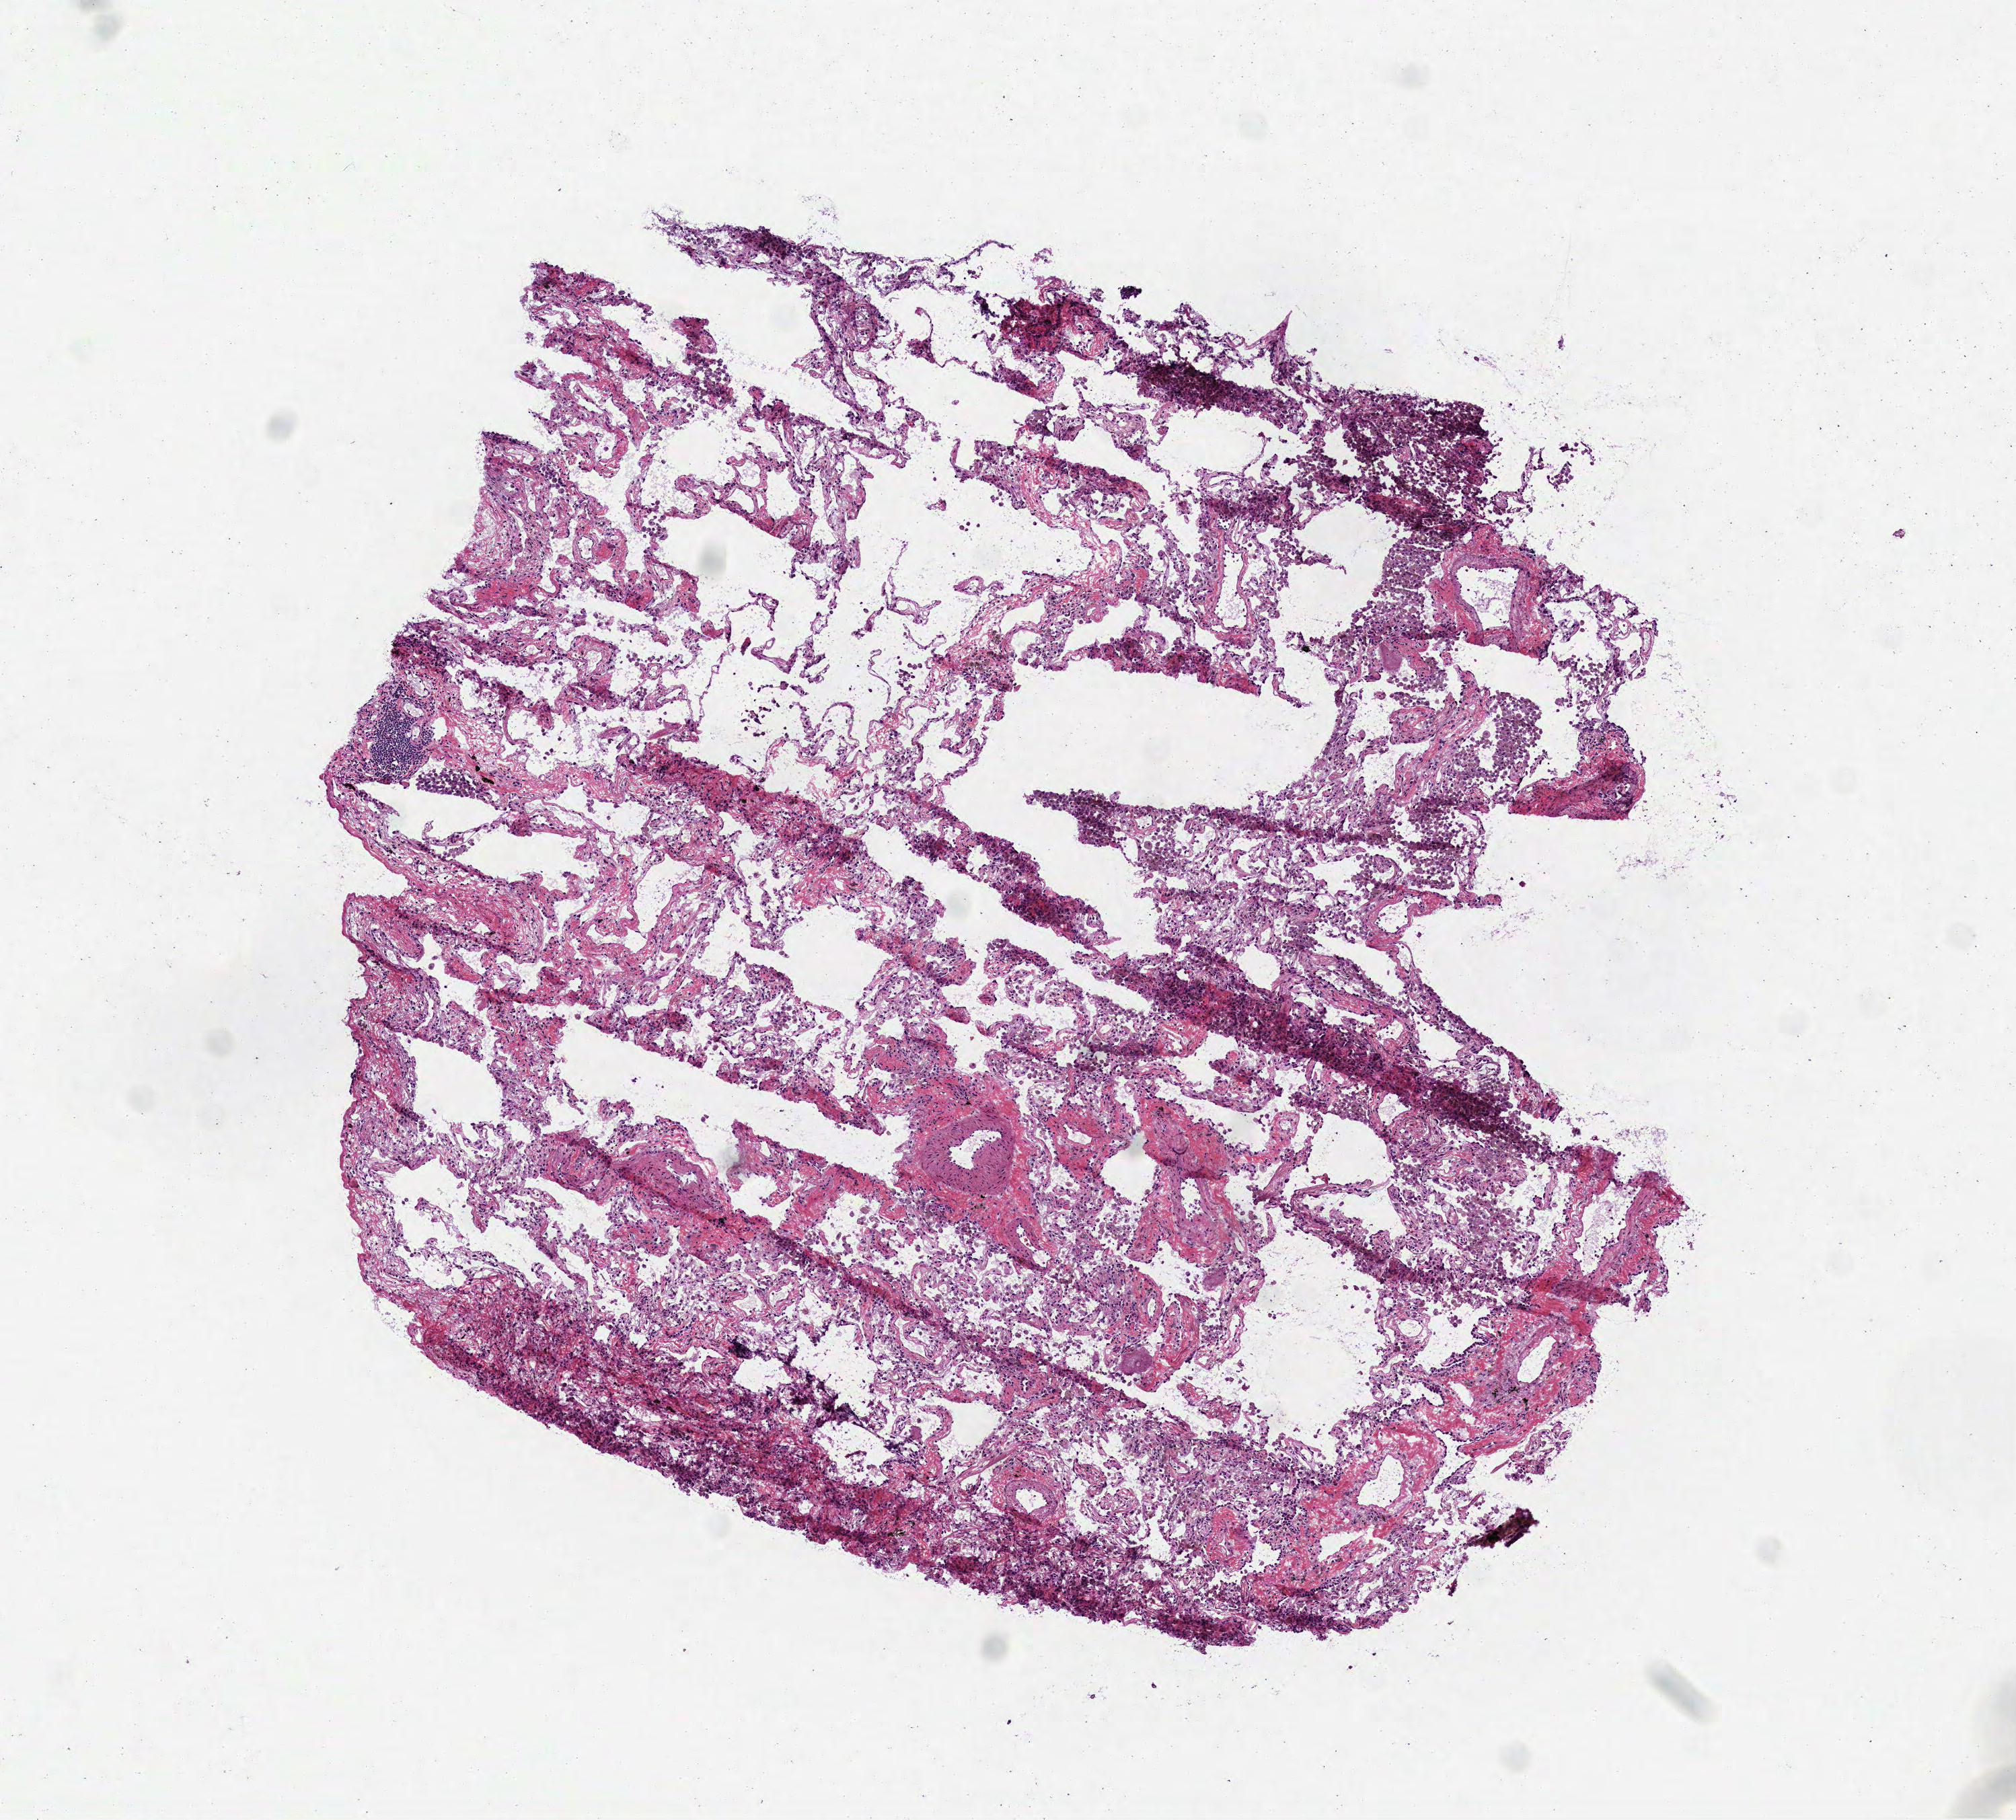
Digitized H&E-stained tissue section (whole slide), low-resolution overview of the scanned area, about 6.0 x 5.5 mm. Frozen section from the top of the tissue portion. Solid tissue normal (non-tumour tissue) sample from the lung. Male, age 73 years at initial diagnosis. Infiltration values recorded for this section: lymphocyte infiltration 5%, monocyte infiltration 30%, neutrophil infiltration 0%.
This section: solid tissue normal sample (biorepository sample class). Patient diagnosis: Adenocarcinoma, NOS.